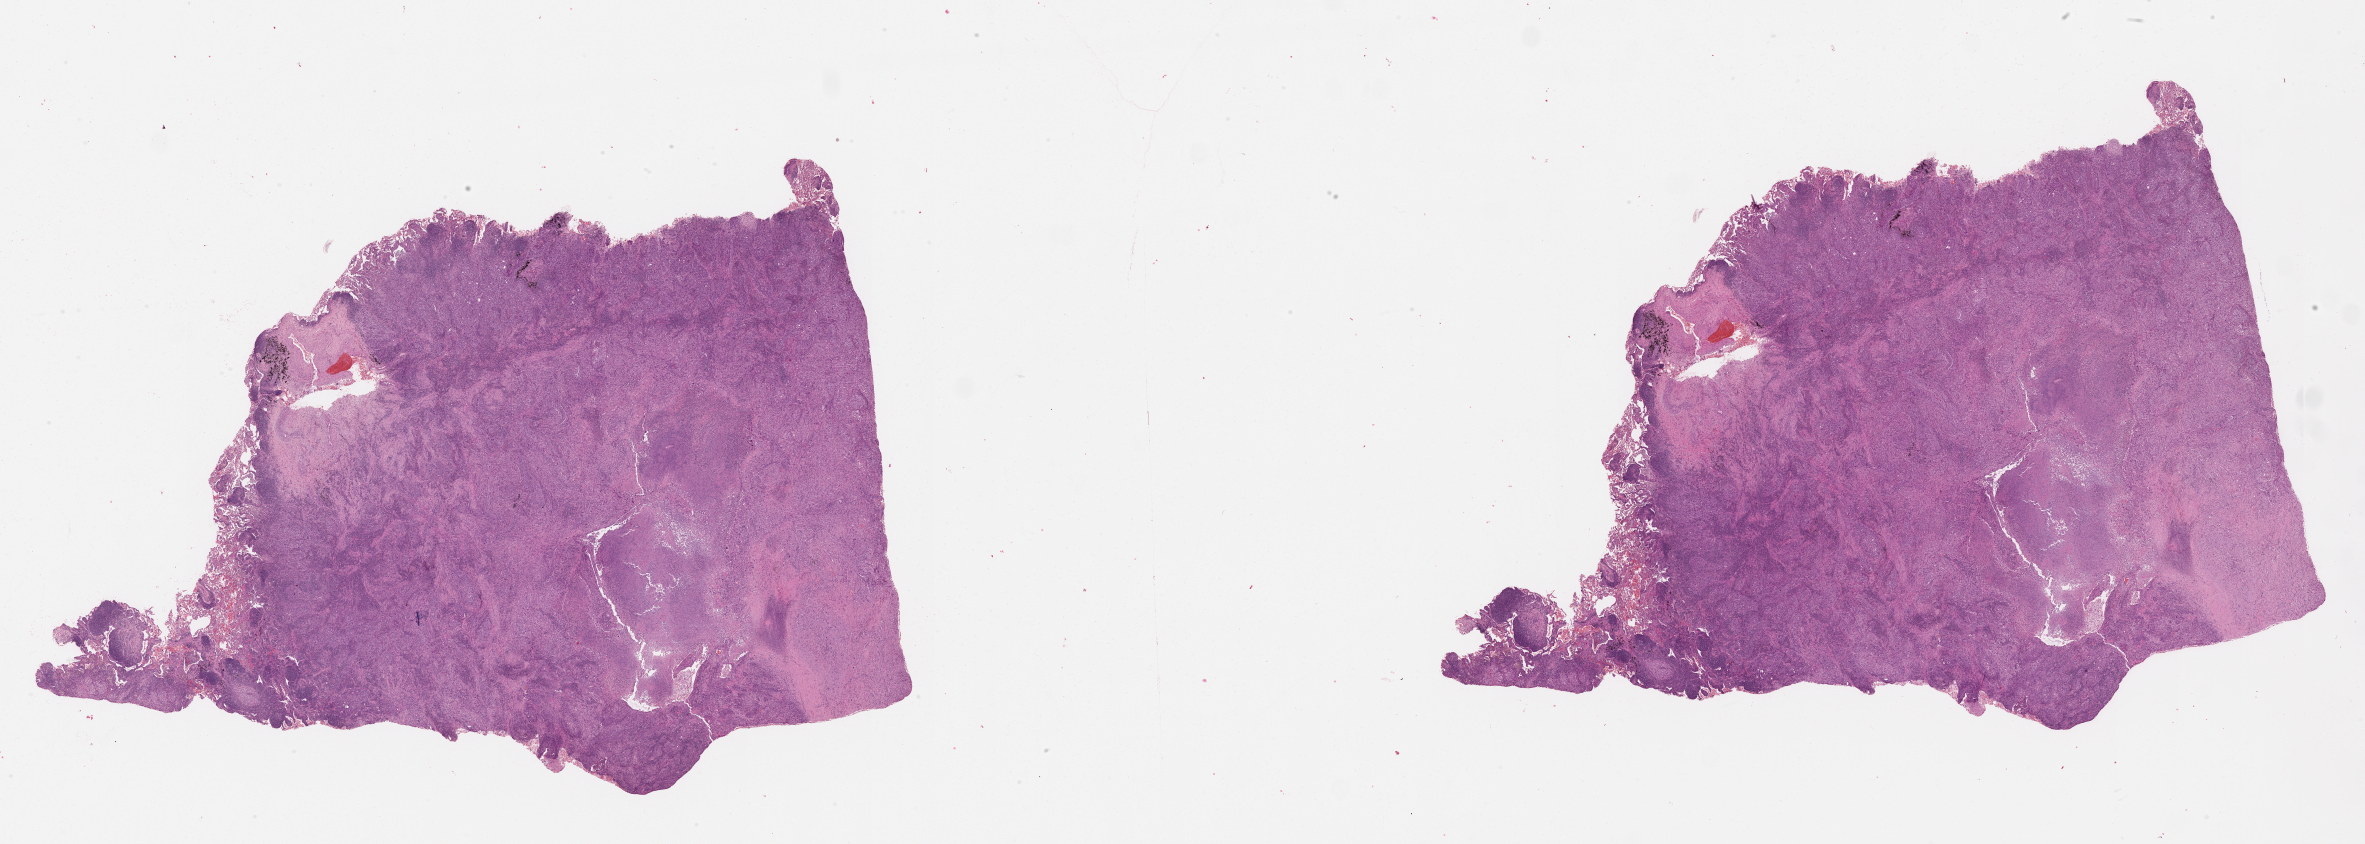
Digitized H&E tissue section (whole slide), shown as a low-resolution overview of the whole scanned area (about 38.1 x 13.6 mm, slide scanned at 20x). Lung, tumour tissue. Patient: male, age 77 years.
• patient diagnosis (cohort enrolment): squamous cell carcinoma (lung)